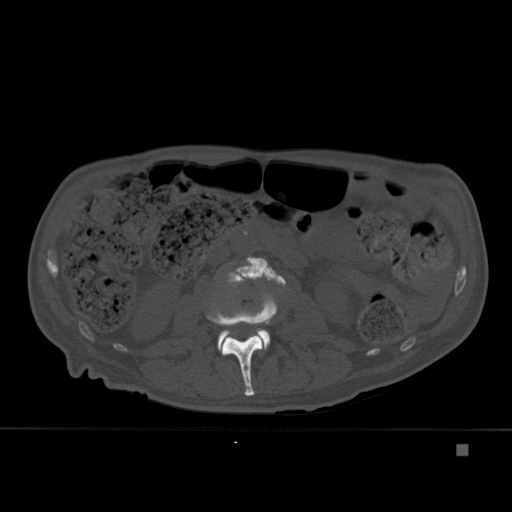
CT including the spine, one axial slice. Slice 155 of 451 in the series (ordered by position). Bone window (W 1800 / L 400 HU). 512 × 512 image matrix. Patient: male, 75 years. From the clinical record (not read from this slice): primary cancer: prostate.
Annotated regions visible in this slice (semi-automatic segmentation, software-assisted and operator-edited):
- L2 vertebra: box from (x=207, y=295) to (x=277, y=396) px
- L3 vertebra: (x=221, y=257)–(x=286, y=350)